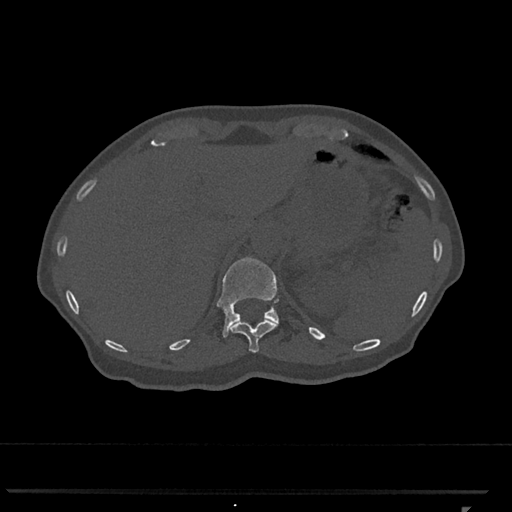
CT including the spine, one axial slice. Slice 490 of 793 in the series (ordered by position). Bone window (W 1800 / L 400 HU). 512 × 512 image matrix. Patient: female, 62 years. Case-level facts recorded for this patient, not image findings: primary cancer: renal.
Annotated regions visible in this slice (semi-automatically segmented with operator editing):
- T11 vertebra: box from (x=230, y=320) to (x=278, y=353) px
- T12 vertebra: (x=216, y=257)–(x=279, y=338)